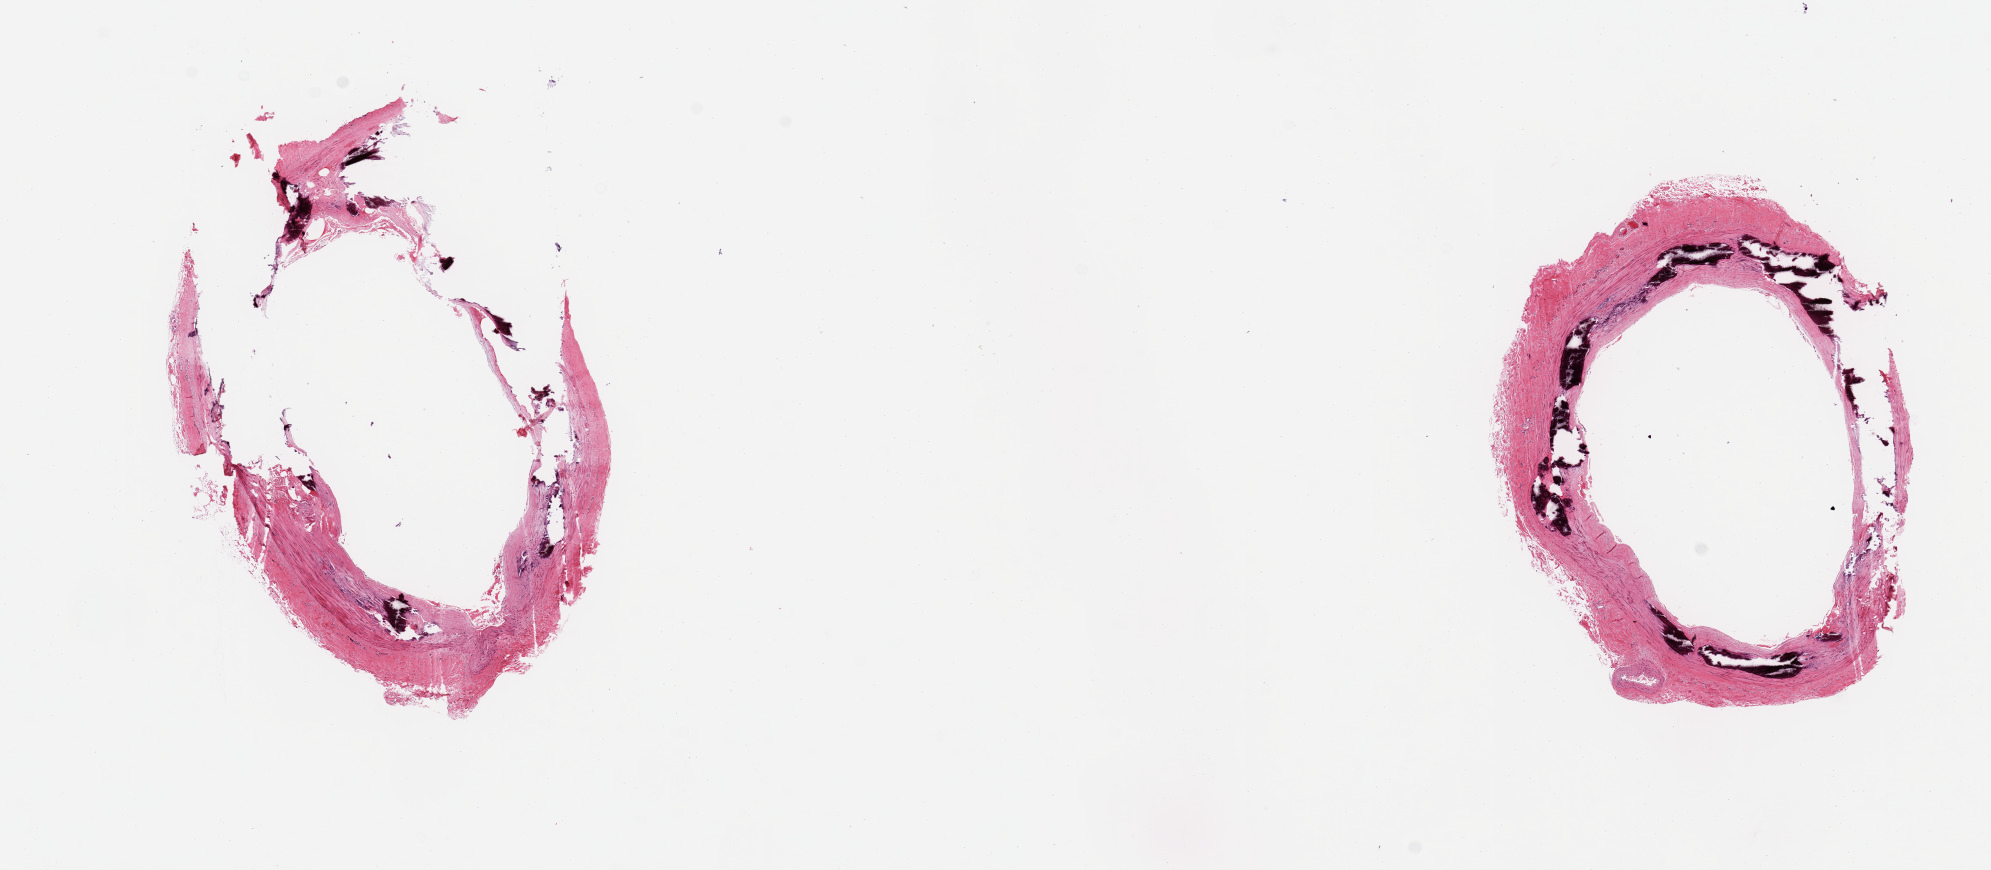
Digitized haematoxylin and eosin-stained section, low-resolution overview of the scanned area, about 15.8 x 6.9 mm (from a 20x scan). PAXgene-fixed paraffin-embedded (PFPE) section. Sampled site (target tissue): tibial artery. Donor tissue sample. Donor: male.
Pathologist's review note for this sample: 2 pieces; Minimal atherosis; prominent Monckeberg medial sclerosis.